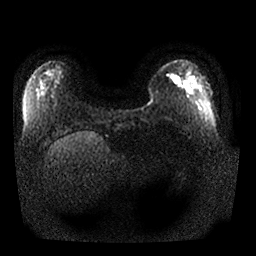
Breast MRI, one axial slice. Position 5 of 25 along the scan axis. Diffusion-weighted series; image 2 of 4 stored at this slice position (different b-values; order by instance number). 1.5 T. 4 mm slice thickness. 256 × 256 image matrix. Female patient.
Outlined on this slice (manually delineated by an expert):
- tumour on diffusion-weighted imaging: bounding box <172,75,181,84> (left, top, right, bottom; pixels)